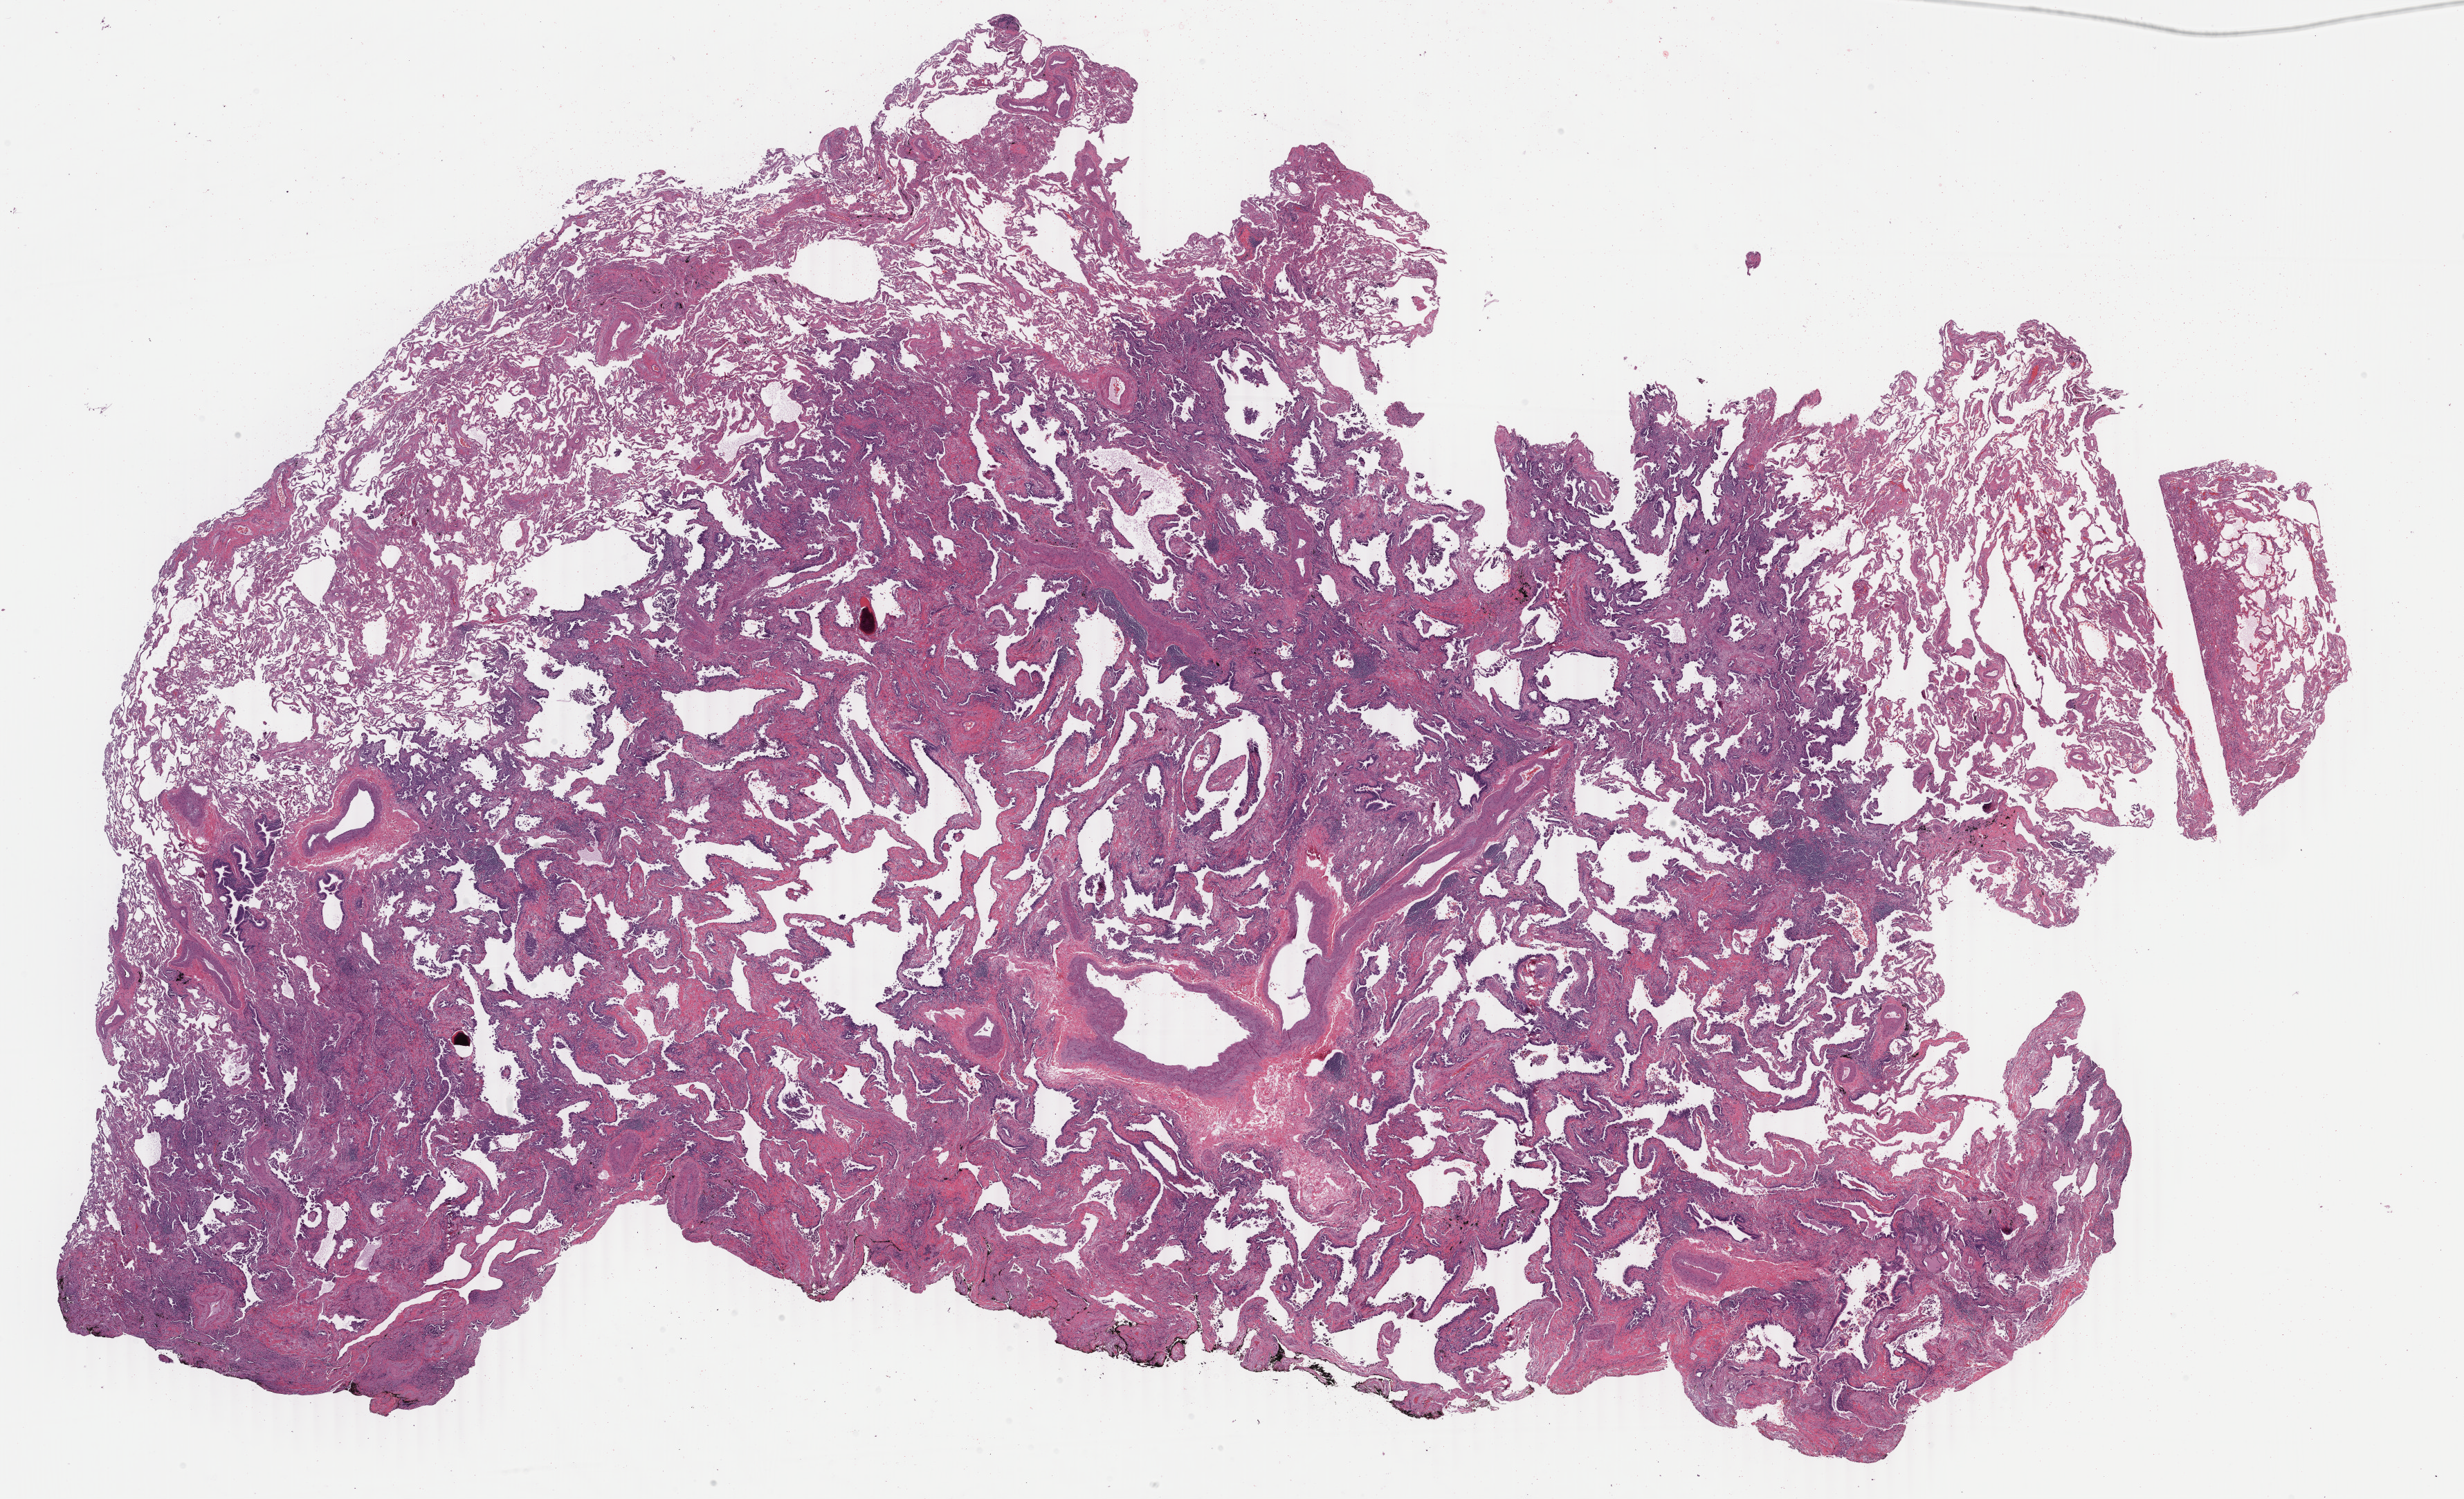
Whole-slide histology image, H&E-stained — a low-resolution overview of the entire scanned area, about 28.3 x 17.2 mm (from a 40x scan); formalin-fixed paraffin-embedded (FFPE) diagnostic section; primary tumour sample from the lung. Patient: male, age at initial diagnosis 81 years.
AJCC pathologic stage: IB (7th edition). Pathologic diagnosis: Adenocarcinoma with mixed subtypes (upper lobe, lung).